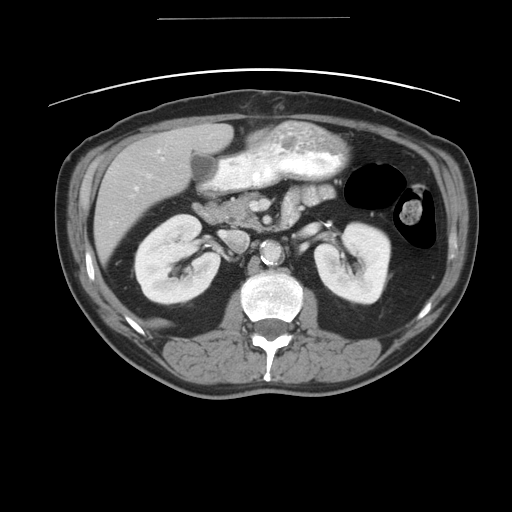
Contrast-enhanced abdominal CT, one axial slice; slice 20 of 49 in the series (ordered by position); reconstruction kernel STANDARD; 120 kVp; soft-tissue window (W 400 / L 40 HU); 5 mm slice thickness; 512 × 512 image matrix, field of view 413 × 413 mm. Male patient, age 57 years. From the clinical record (not read from this slice): diagnosis: colorectal cancer liver metastases, imaged before liver resection; multiple liver metastases: yes.
Outlined on this slice (manually delineated by an expert):
- hepatic veins: bounding box [x1, y1, x2, y2] px = [146, 173, 149, 176]
- liver: [94, 124, 232, 263]
- planned liver remnant (the part of the liver to remain after resection): [215, 125, 232, 149]
- portal vein (with intrahepatic branches): [134, 186, 137, 189]